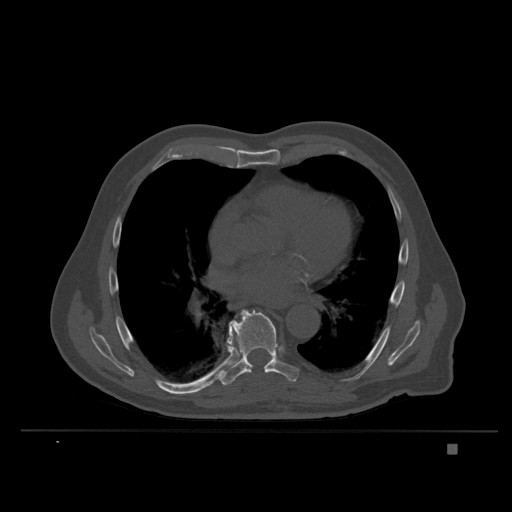
CT including the spine, one axial slice; position 232 of 435 along the scan axis; bone window (W 1800 / L 400 HU); 1.5 mm slice thickness; 512 × 512 image matrix, field of view 434 × 434 mm. Male patient, age 73 years. From the clinical record (not read from this slice): primary cancer: skin.
Structures marked on this image (semi-automatically segmented with operator editing):
- T7 vertebra: box from (x=228, y=321) to (x=234, y=342) px
- T8 vertebra: (x=219, y=309)–(x=299, y=386)